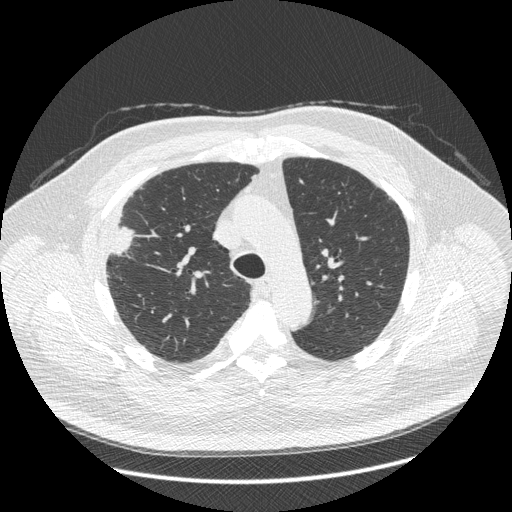
Low-dose screening chest CT, one axial slice. Position 308 of 426 along the scan axis. 120 kVp. Lung window (W 1500 / L -600 HU). 512 × 512 image matrix, field of view 400 × 400 mm.
Structures marked on this image (outlined manually by an expert reader):
- lesion 1 (tumor, upper lobe of right lung): bounding box <111,227,134,255> (left, top, right, bottom; pixels)